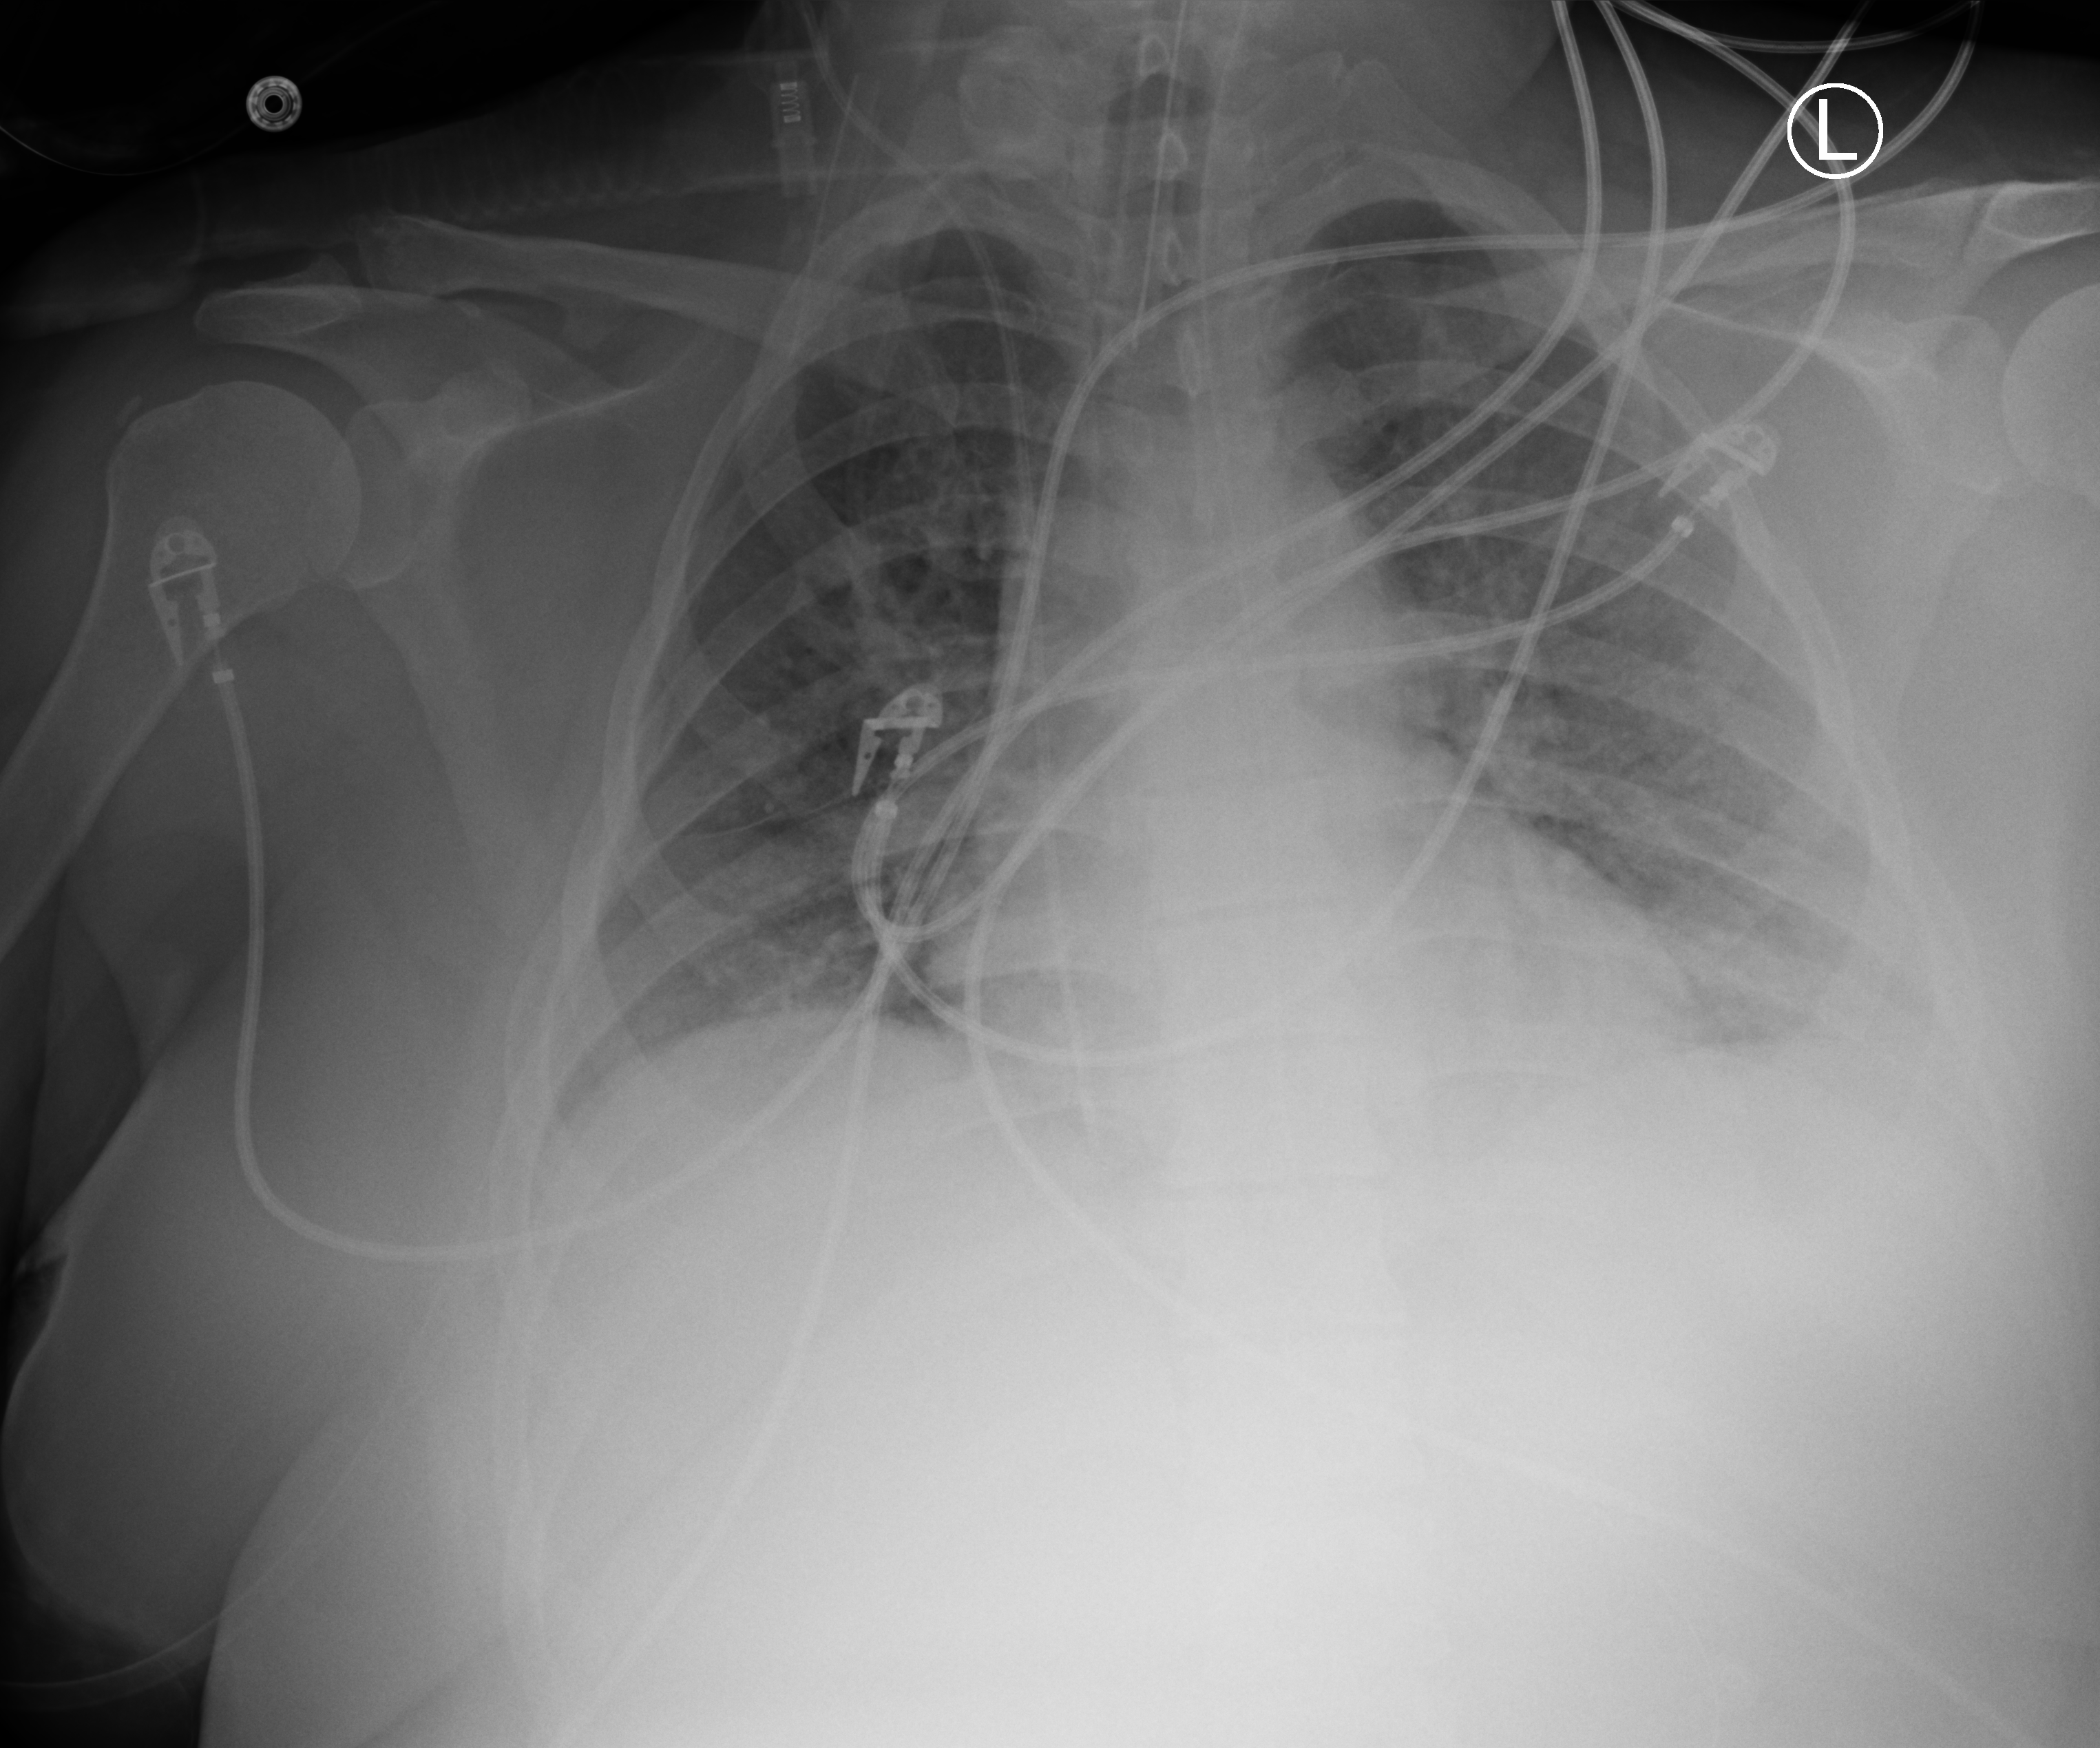
Chest X-ray (portable). Patient hospitalised with COVID-19; female, aged 18–59 years.
Admission-level facts for this patient (not findings on this image; timing relative to this image not recorded): mechanically ventilated during this hospital stay: yes; COPD (admission record): no.